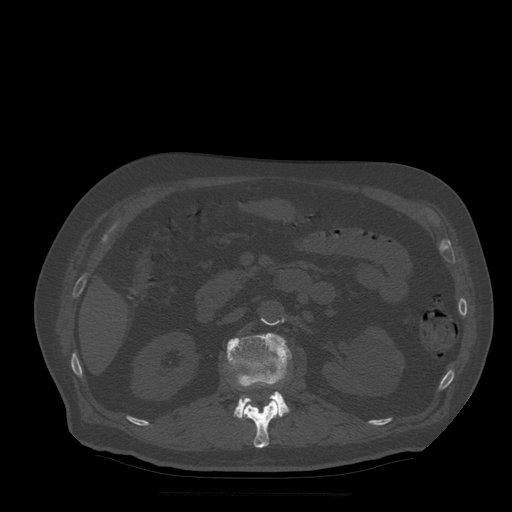
CT including the spine, one axial slice; position 183 of 522 along the scan axis; bone window (W 1800 / L 400 HU); 1.25 mm slice thickness; 512 × 512 image matrix, field of view 420 × 420 mm. Patient age 72 years. Case-level facts recorded for this patient, not image findings: primary cancer: prostate.
Annotated regions visible in this slice (semi-automatically segmented with operator editing):
- L1 vertebra: bounding box [x1, y1, x2, y2] px = [239, 373, 279, 448]
- L2 vertebra: [227, 333, 292, 419]